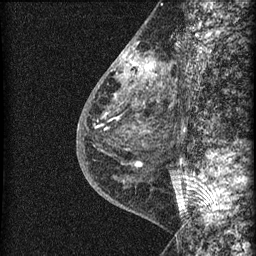
Breast MRI (dynamic contrast-enhanced), one sagittal slice. Slice 25 of 60 in the series (ordered by position). Dynamic contrast-enhanced series, image 2 of 3 at this slice position (ordered by acquisition). 1.5 T. TE 4.2 ms, TR 22.7 ms. 1.5 mm slice thickness. 256 × 256 image matrix, field of view 180 × 180 mm. Female patient, age 48 years. Case-level facts recorded for this patient, not image findings: setting: breast cancer imaged before/during neoadjuvant chemotherapy; receptor status: triple-negative.
Outlined on this slice (semi-automatic segmentation, software-assisted and operator-edited):
- analysis volume of interest (the breast-tissue region the enhancement analysis was run in; not a lesion): bounding box [x1, y1, x2, y2] px = [115, 34, 169, 162]
- tumour enhancement mask (voxels above the 90 % enhancement threshold inside the analysis volume of interest): [119, 47, 156, 79]